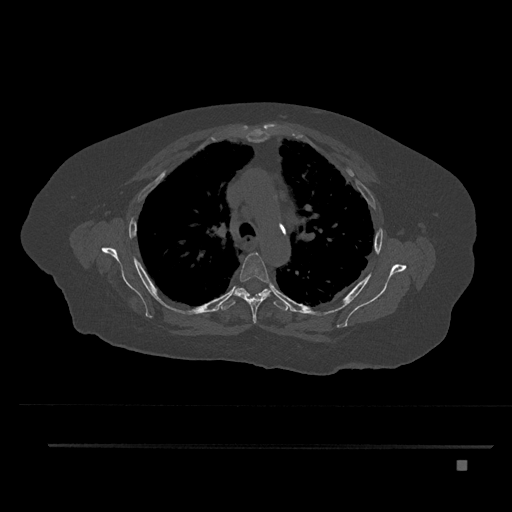
CT including the spine, one axial slice; position 591 of 797 along the scan axis; 120 kVp; bone window (W 1800 / L 400 HU); 0.5 mm slice thickness; 512 × 512 image matrix. Patient: female, 76 years. From the clinical record (not read from this slice): primary cancer: lung; vertebrae with lytic lesions (as recorded): T11, L3.
Structures marked on this image (semi-automatically segmented with operator editing):
- T4 vertebra: box from (x=234, y=252) to (x=272, y=323) px
- T5 vertebra: (x=219, y=287)–(x=289, y=311)